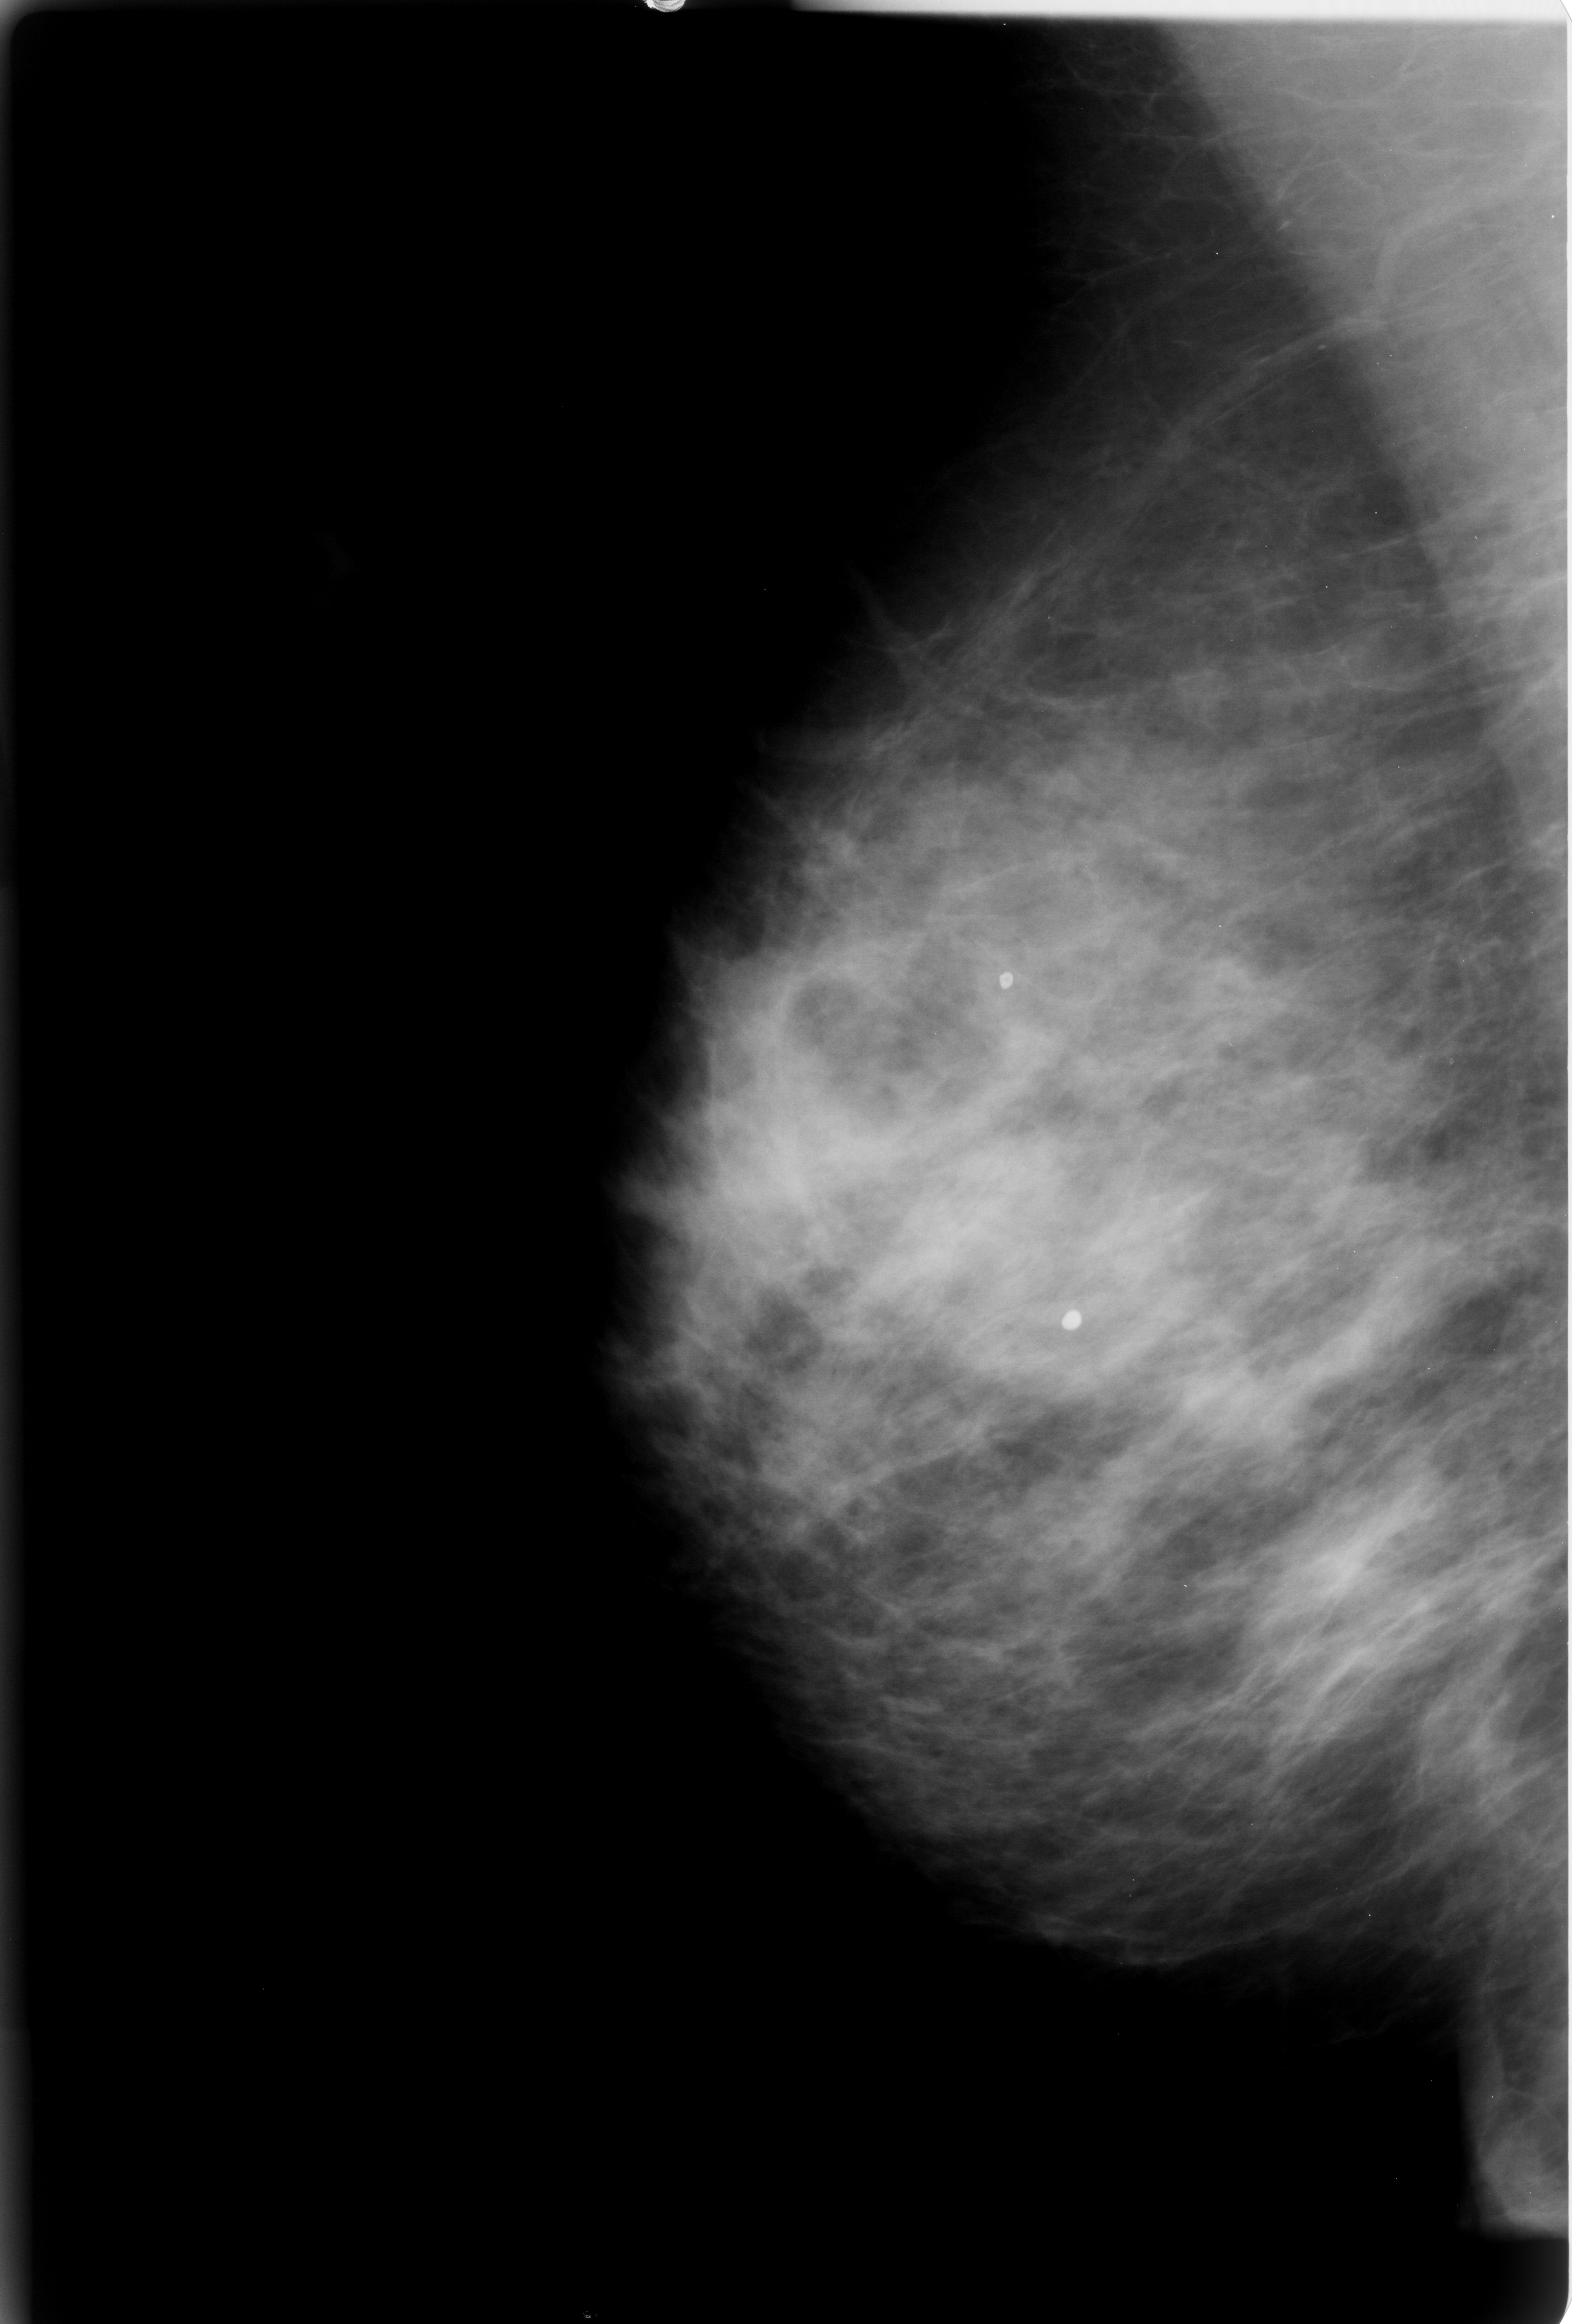
Mammogram (digitized film); right breast; MLO view; BI-RADS breast density category 3 (scale 1–4); 1572 × 2324 image matrix.
Expert-marked regions of interest on this image (one box per marked abnormality):
- Finding 1 of 2: calcifications, morphology coarse / round and regular / lucent centered; BI-RADS assessment category 2; benign; no additional work-up was recommended (outcome (as recorded, no biopsy): benign without callback): bounding box [x1, y1, x2, y2] px = [984, 959, 1030, 1006]
- Finding 2 of 2: calcifications, morphology coarse / round and regular / lucent centered; BI-RADS assessment category 2; subtlety rating 4 on a 1 (subtle) to 5 (obvious) scale; outcome (as recorded, no biopsy): benign without callback (not worked up further): [1053, 1294, 1091, 1337]